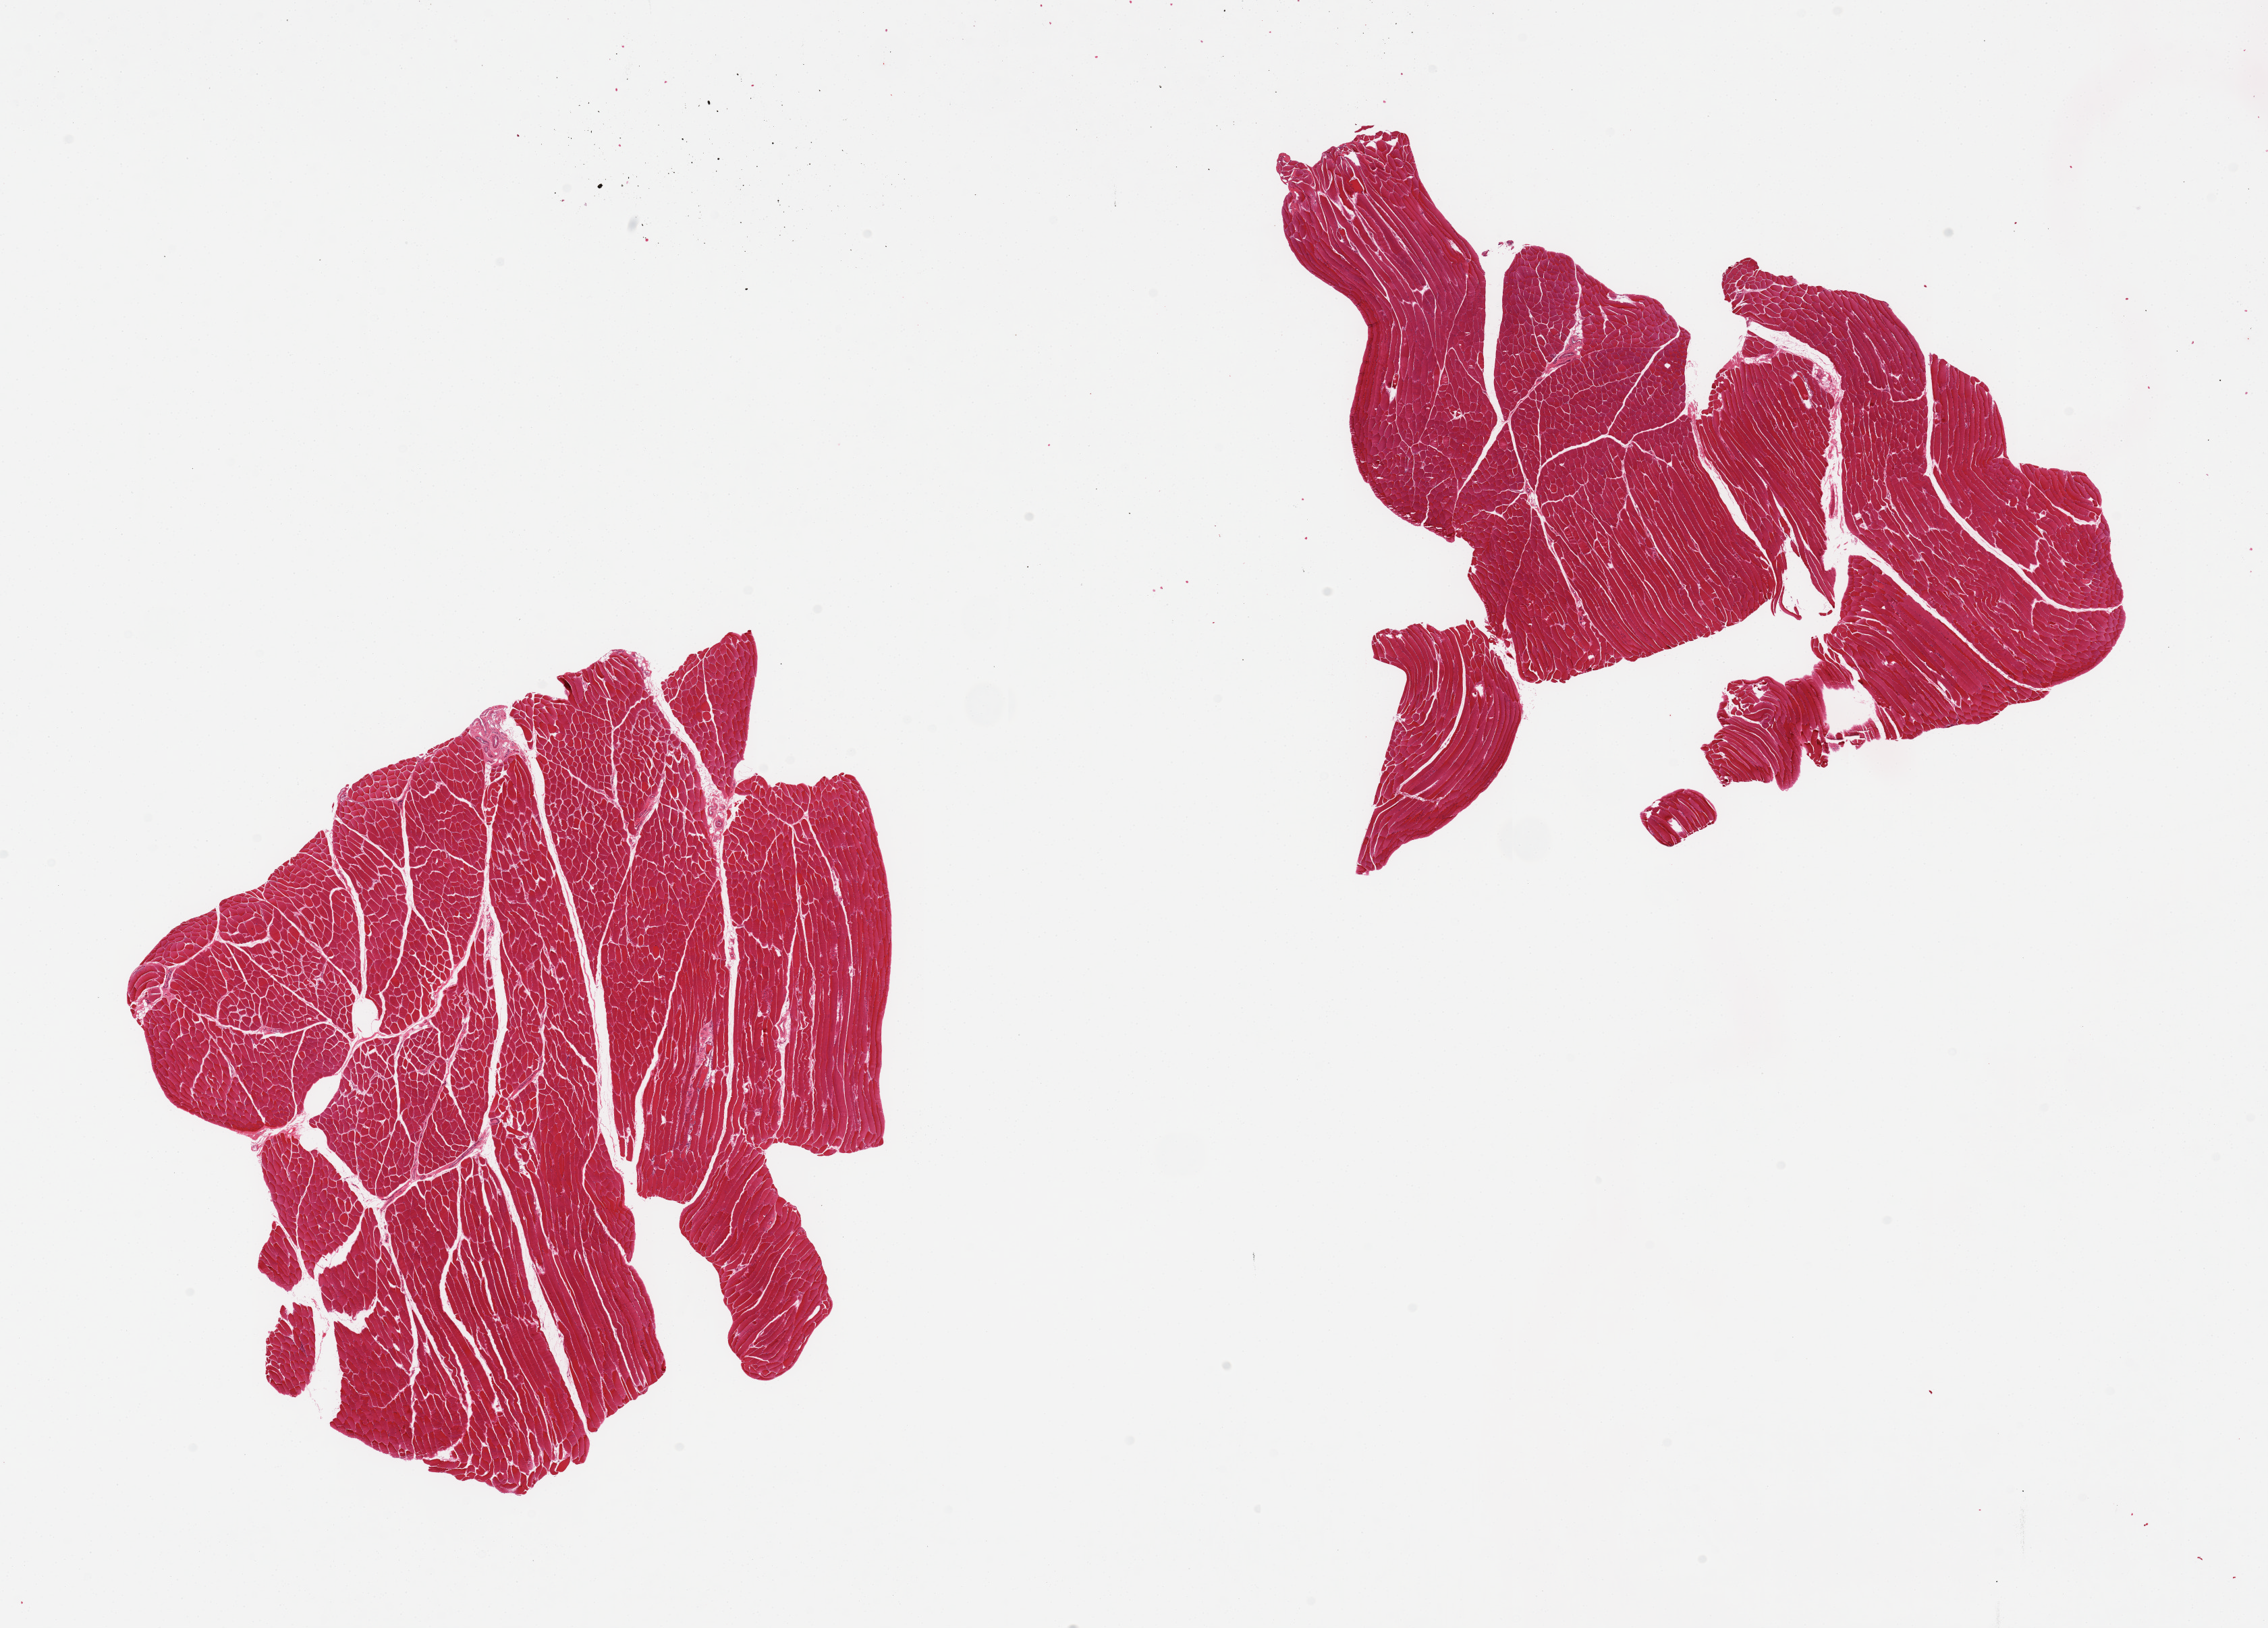
Haematoxylin and eosin whole-slide image — low-resolution overview of the scanned area, about 26.6 x 19.1 mm (slide scanned at 20x). PAXgene-fixed paraffin-embedded (PFPE) section. Target tissue: skeletal muscle. Tissue donor sample. Donor sex: male.
* reviewer comment on this tissue sample: 2 pieces